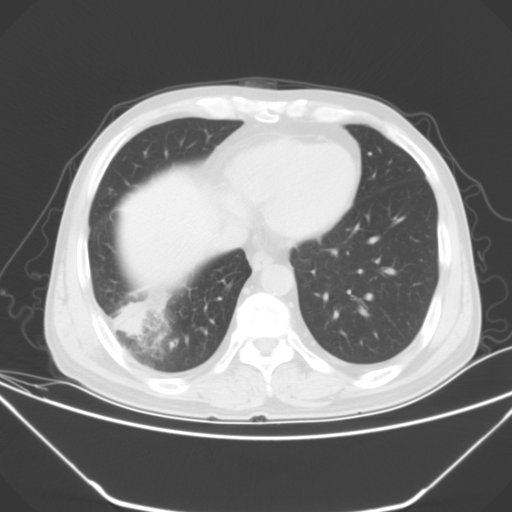
Chest CT, one axial slice; position 14 of 52 along the scan axis; 120 kVp; lung window (W 1500 / L -600 HU); 5 mm slice thickness; 512 × 512 image matrix. Patient: male, 54 years. From the clinical record (not read from this slice): clinical TNM (as recorded): T2 N1 M0; histopathological grade: G3.
Outlined on this slice (bounding box drawn by a radiologist):
- lung tumour (recorded histology: adenocarcinoma): bounding box (x1, y1, x2, y2) in pixels: (112, 303, 149, 336)